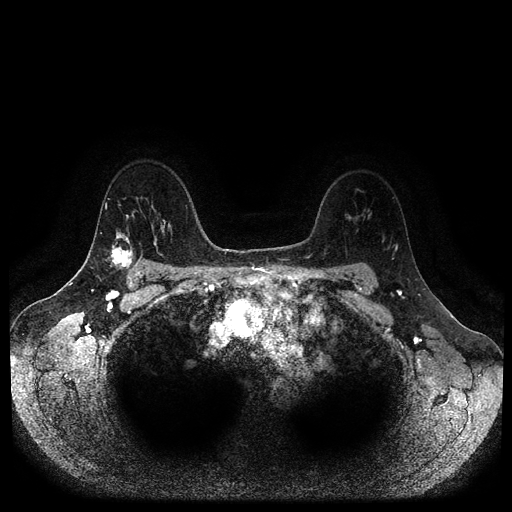
Breast MRI (dynamic contrast-enhanced, multi-phase), one axial slice; slice 74 of 116 in the series (ordered by position); dynamic contrast-enhanced series, time point 2 of 5 at this slice position (early post-contrast); 1.5 T; TE 2.6 ms, TR 5.3 ms; 512 × 512 image matrix, field of view 360 × 360 mm. Patient: female, 45 years.
Annotated regions visible in this slice (semi-automatically segmented with operator editing):
- breast lesion (labelled 'tumour' in the annotation; benign lesions carry a separate 'benign' label): bounding box <110,242,135,271> (left, top, right, bottom; pixels)